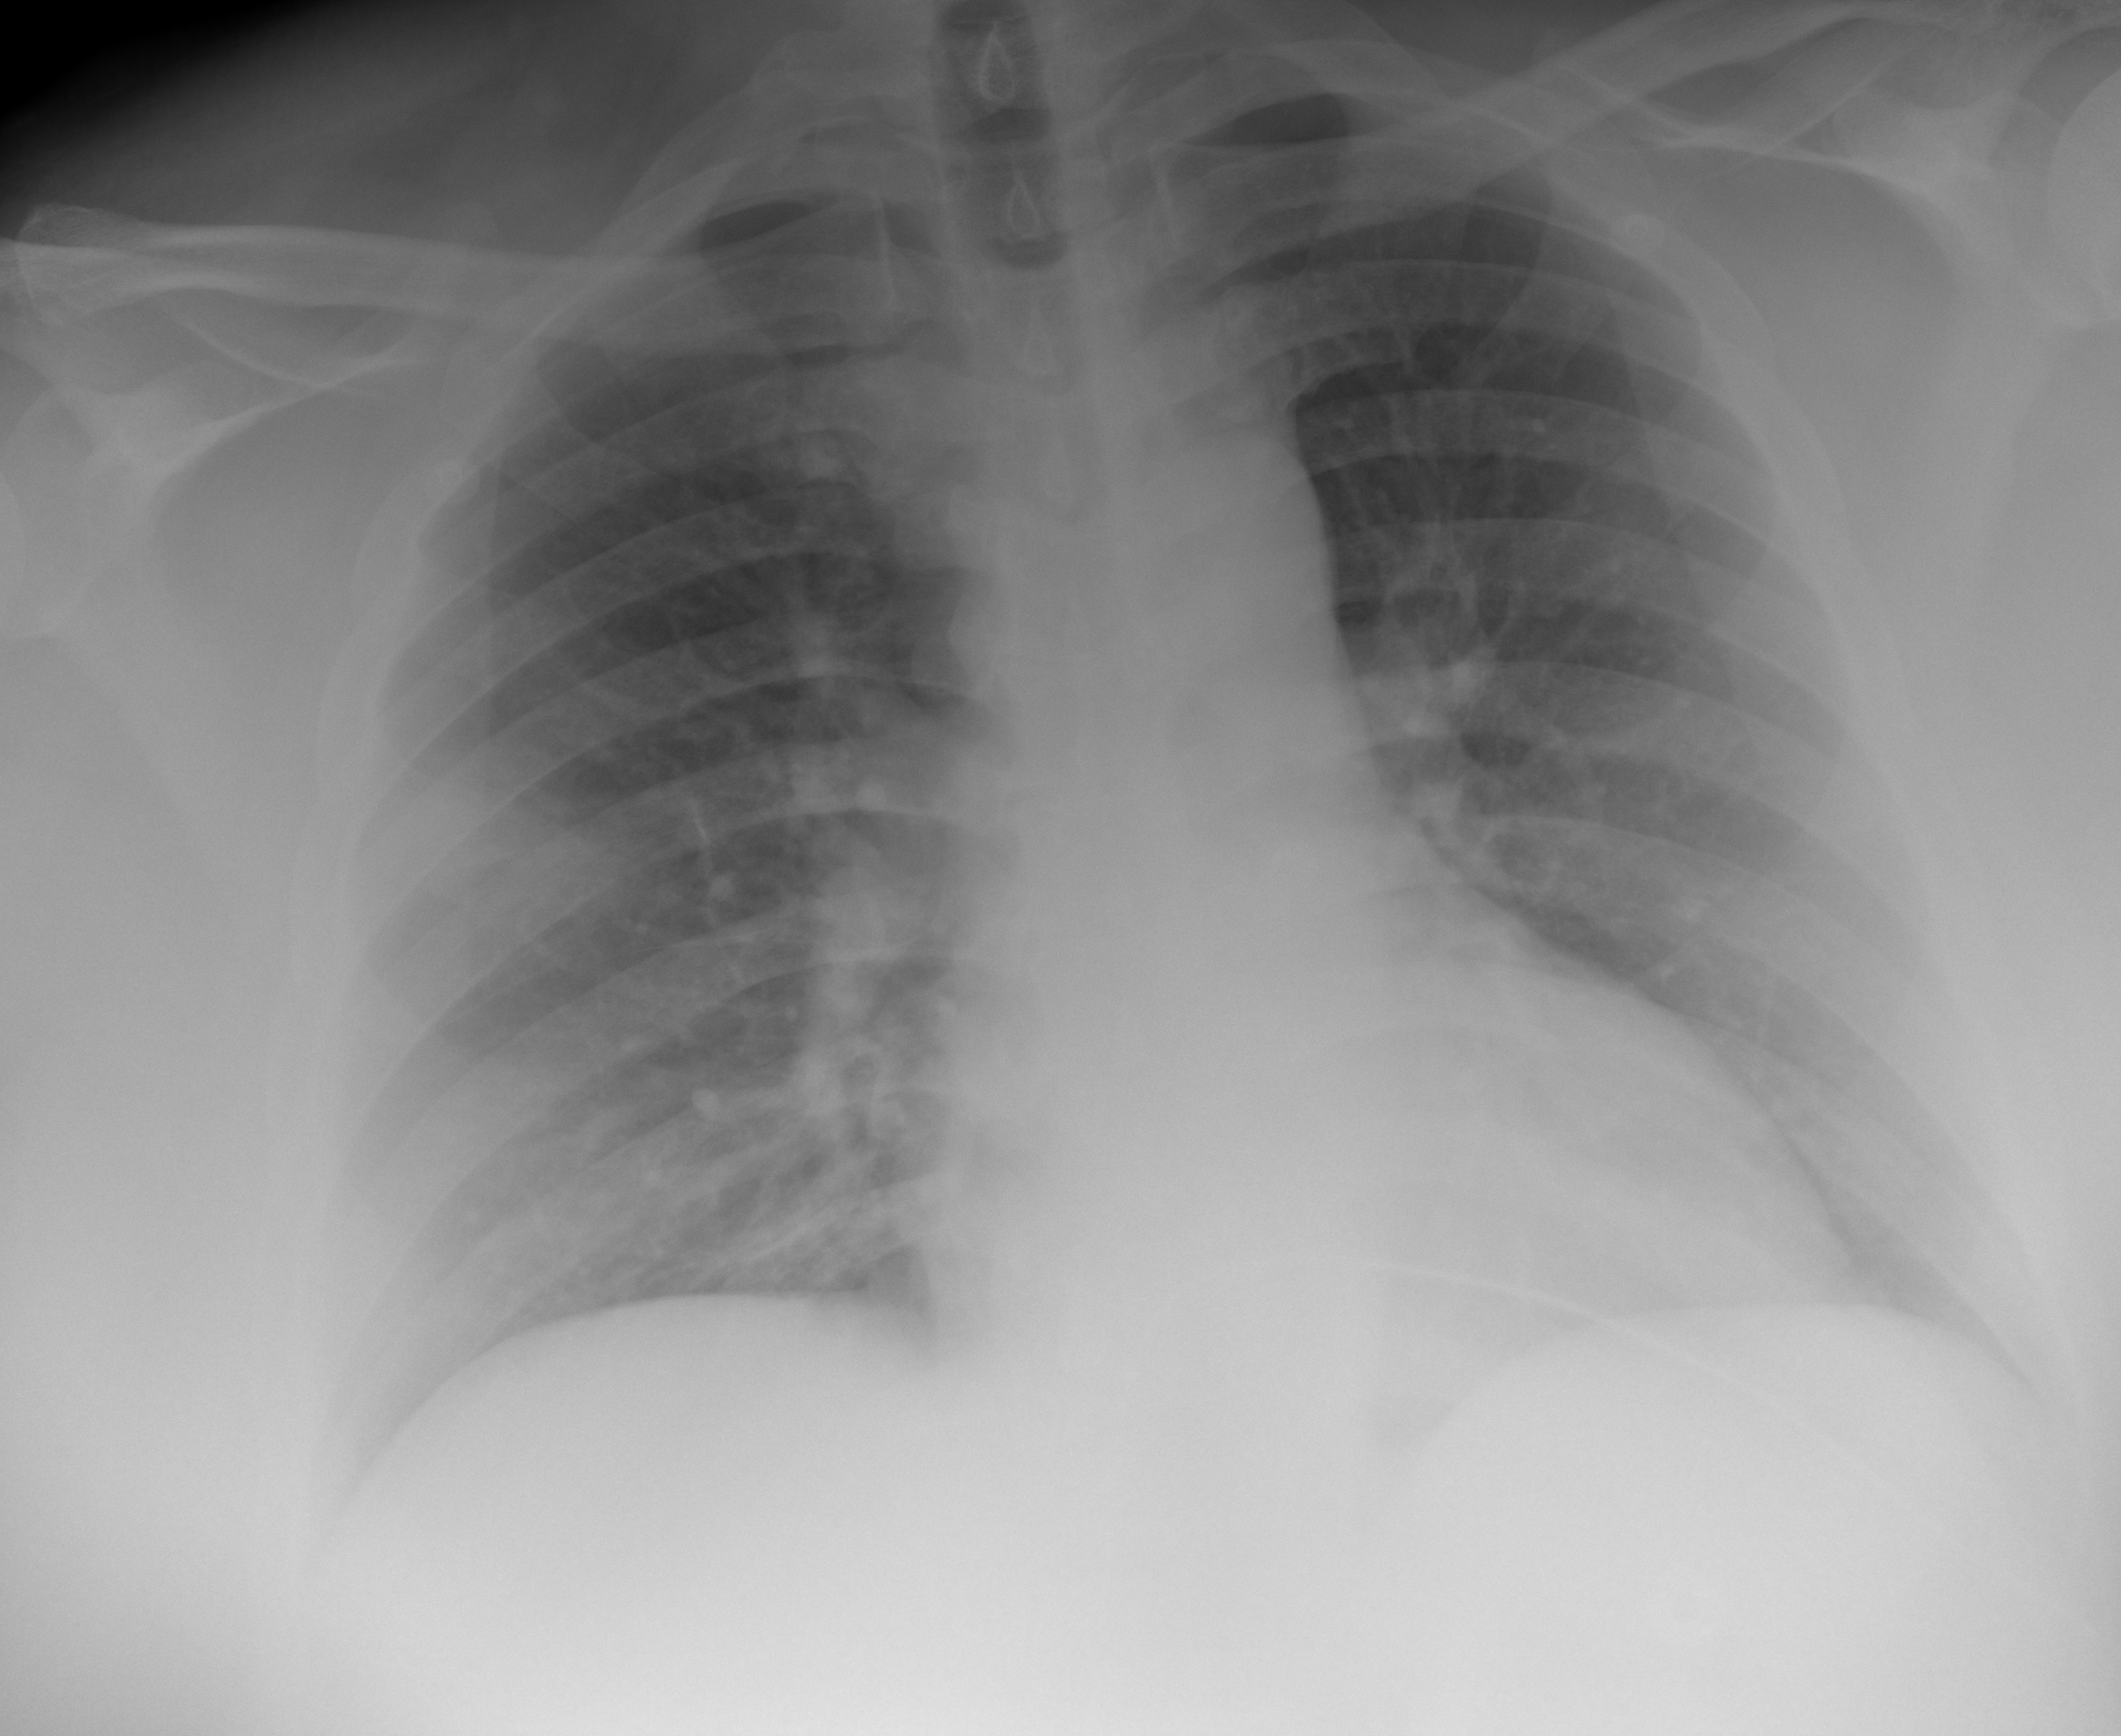
Chest X-ray (portable), AP projection. Male patient, age 47 years; imaged 0 days after the COVID-19 diagnosis.
Key findings recorded by the radiologist: The lungs are clear without evidence of focal consolidation.